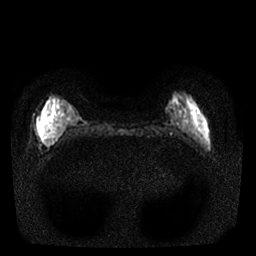
Breast MRI, one axial slice; position 4 of 25 along the scan axis; diffusion-weighted series; image 2 of 4 stored at this slice position (different b-values; order by instance number); 1.5 T; 4 mm slice thickness; 256 × 256 image matrix, field of view 310 × 310 mm. Female patient.
Annotated regions visible in this slice (outlined manually by an expert reader):
- tumour on diffusion-weighted imaging: box from (x=40, y=118) to (x=45, y=127) px